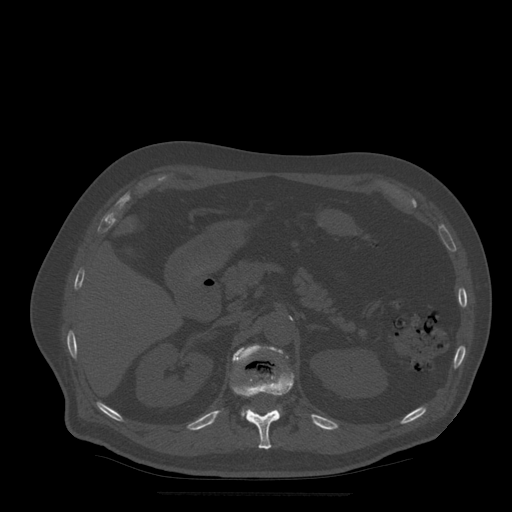
CT including the spine, one axial slice. Slice 212 of 522 in the series (ordered by position). Bone window (W 1800 / L 400 HU). 1.25 mm slice thickness. 512 × 512 image matrix, field of view 420 × 420 mm. Patient age 72 years. From the clinical record (not read from this slice): primary cancer: prostate.
Outlined on this slice (semi-automatic segmentation, software-assisted and operator-edited):
- L1 vertebra: bounding box (x1, y1, x2, y2) in pixels: (233, 345, 288, 418)
- T12 vertebra: (232, 372, 294, 449)